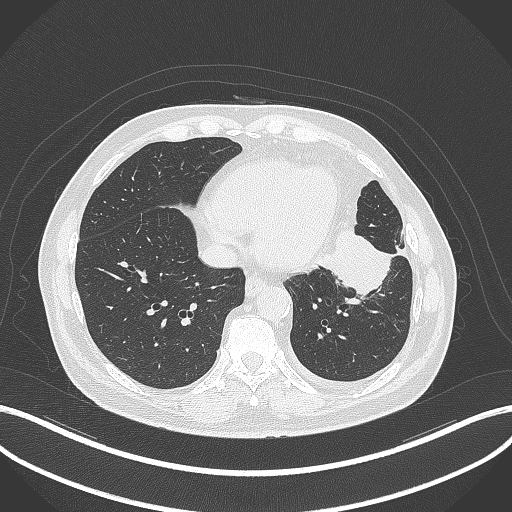
Chest CT, one axial slice; slice 110 of 230 in the series (ordered by position); reconstruction kernel B70f; 120 kVp; lung window (W 1500 / L -600 HU); 512 × 512 image matrix, field of view 400 × 400 mm. Patient: male, 68 years. From the clinical record (not read from this slice): clinical TNM (as recorded): T2b N0 M0.
Annotated regions visible in this slice (bounding box drawn by a radiologist):
- lung tumour (recorded histology: squamous cell carcinoma): box from (x=315, y=221) to (x=397, y=300) px